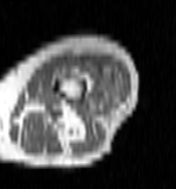
MRI of an extremity soft-tissue mass, one axial slice; MR volume resampled by the dataset authors to the PET/CT grid (not the native acquisition matrix); 3.27 mm slice thickness; 176 × 189 image matrix, field of view 172 × 185 mm. Female patient. Case-level facts recorded for this patient, not image findings: histological type: undifferentiated – high grade; grade: high; site of the primary tumour: left thigh.
Outlined on this slice (expert contour drawn on MRI and transferred to this co-registered scan by the dataset authors):
- gross tumour volume including surrounding oedema: bounding box (x1, y1, x2, y2) in pixels: (66, 59, 120, 104)